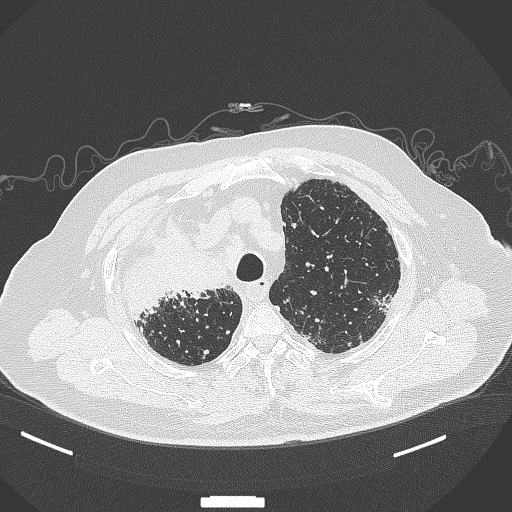
Chest CT, one axial slice. Slice 289 of 384 in the series (ordered by position). 120 kVp. Lung window (W 1500 / L -600 HU). 512 × 512 image matrix. Patient: male, 69 years. From the clinical record (not read from this slice): clinical TNM (as recorded): T4 N3 M1.
Annotated regions visible in this slice (rectangle marked by the reading radiologist):
- lung tumour (recorded histology: adenocarcinoma): bounding box <119,210,233,325> (left, top, right, bottom; pixels)